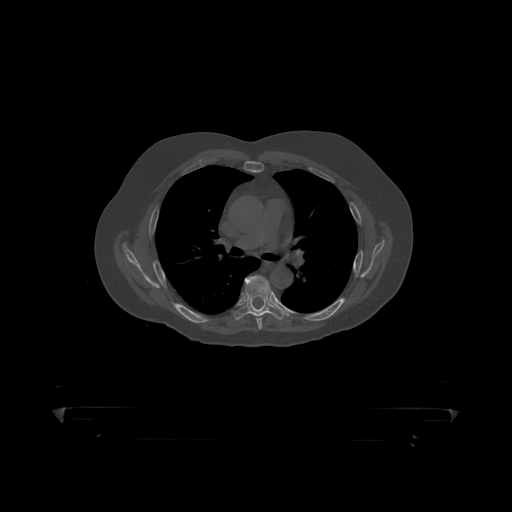
CT including the spine, one axial slice. Slice 306 of 390 in the series (ordered by position). Reconstruction kernel STANDARD. 120 kVp. Bone window (W 1800 / L 400 HU). 1.25 mm slice thickness. 512 × 512 image matrix, field of view 650 × 650 mm. Male patient, age 60 years. Case-level facts recorded for this patient, not image findings: primary cancer: prostate.
Structures marked on this image (semi-automatically segmented with operator editing):
- T6 vertebra: bounding box [x1, y1, x2, y2] px = [235, 276, 283, 319]